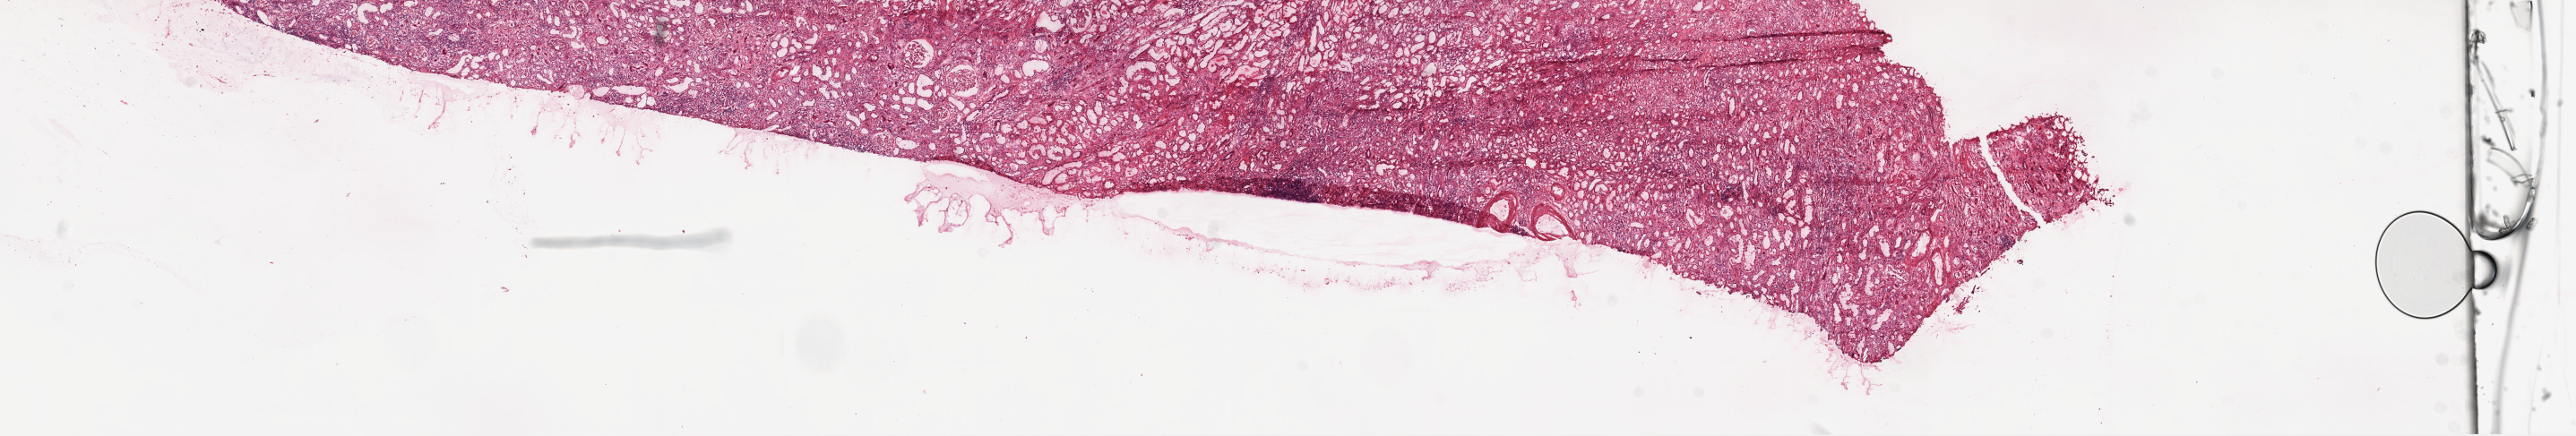
Whole-slide histology image, Hematoxylin and eosin (H&E) stained, a low-resolution overview of the entire scanned area, about 23.1 x 3.9 mm, frozen section from the top of the tissue portion, solid tissue normal (non-tumour tissue) sample from the kidney. Female, age 68 years at initial diagnosis.
• this section: solid tissue normal sample (biorepository sample class)
• patient diagnosis: Clear cell adenocarcinoma, NOS